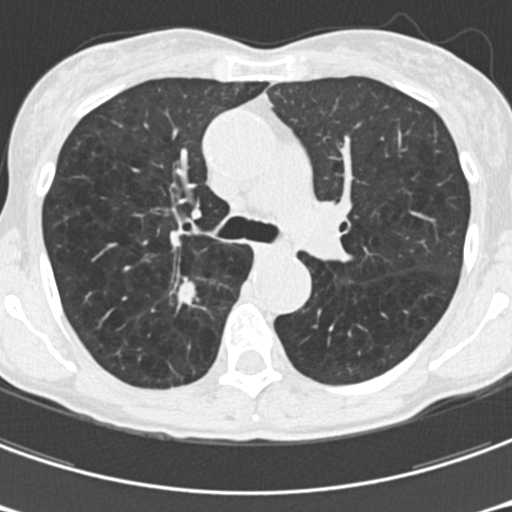
Low-dose screening chest CT, one axial slice; slice 112 of 176 in the series (ordered by position); 120 kVp; lung window (W 1500 / L -600 HU); 2 mm slice thickness; 512 × 512 image matrix.
Annotated regions visible in this slice (outlined manually by an expert reader):
- lesion 1 (tumor, upper lobe of right lung): box from (x=175, y=276) to (x=198, y=309) px